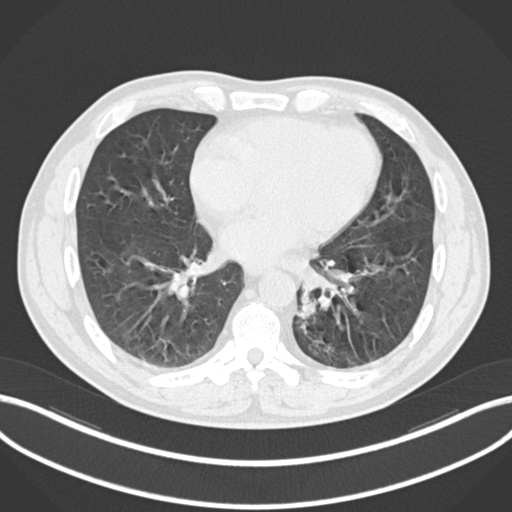
Chest CT, one axial slice. Reconstruction kernel B30f. 120 kVp. Lung window (W 1500 / L -600 HU). 512 × 512 image matrix, field of view 400 × 400 mm. Male patient, age 50 years. From the clinical record (not read from this slice): clinical TNM (as recorded): T2a N3 M0.
Outlined on this slice (rectangle marked by the reading radiologist):
- lung tumour (recorded histology: squamous cell carcinoma): bounding box [x1, y1, x2, y2] px = [289, 288, 322, 322]